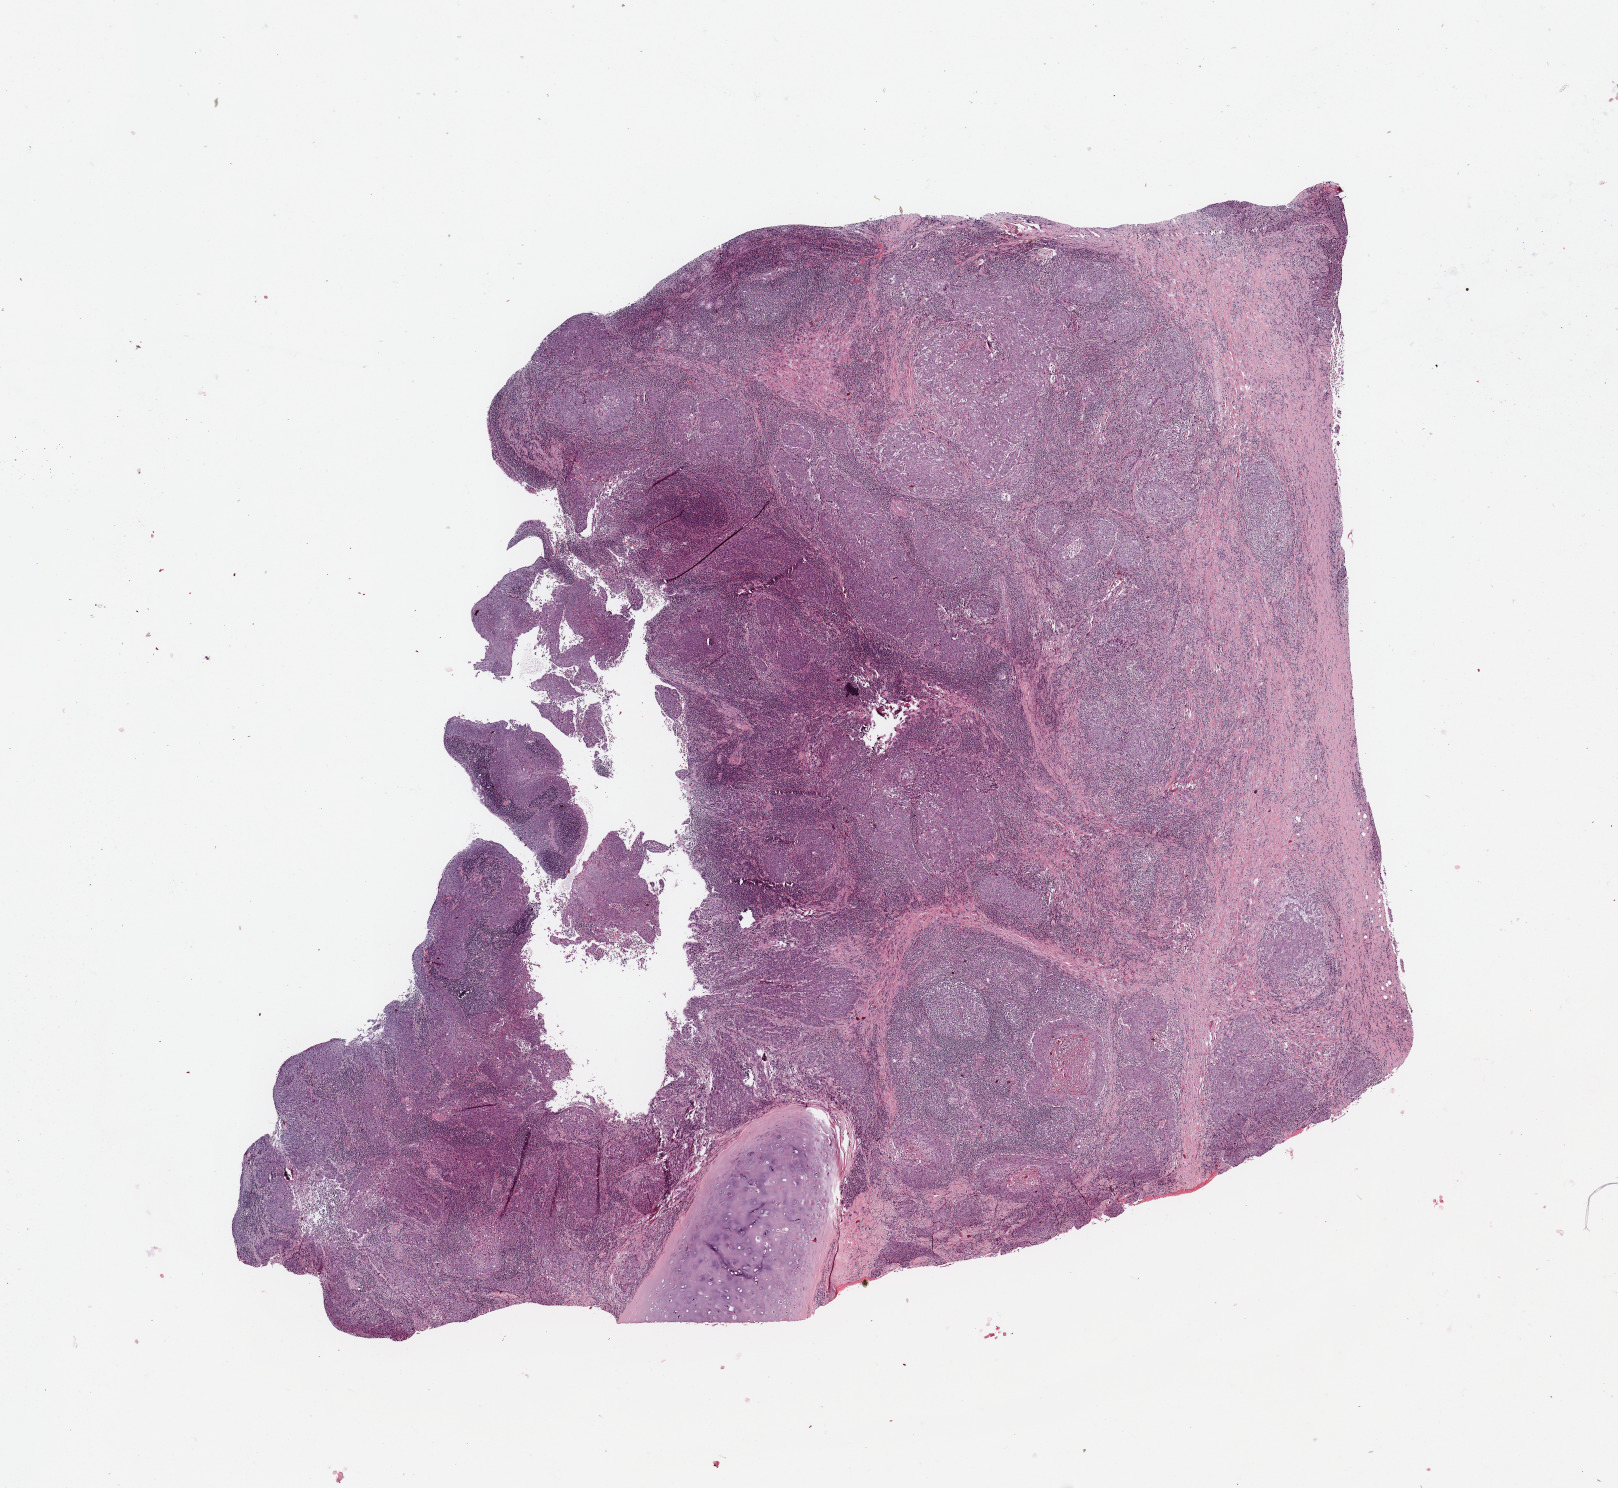
H&E whole-slide image — whole scanned area (about 12.8 x 11.8 mm) shown as a low-resolution overview; tumour tissue sample, sampled site: lung. 66-year-old male patient. Histologic grade: G3 (poorly differentiated). Pathologist review of this section (percent, as recorded): tumour nuclei 75%, necrosis 5%.
- histologic diagnosis: Squamous cell carcinoma, NOS
- AJCC pathologic stage: IIA